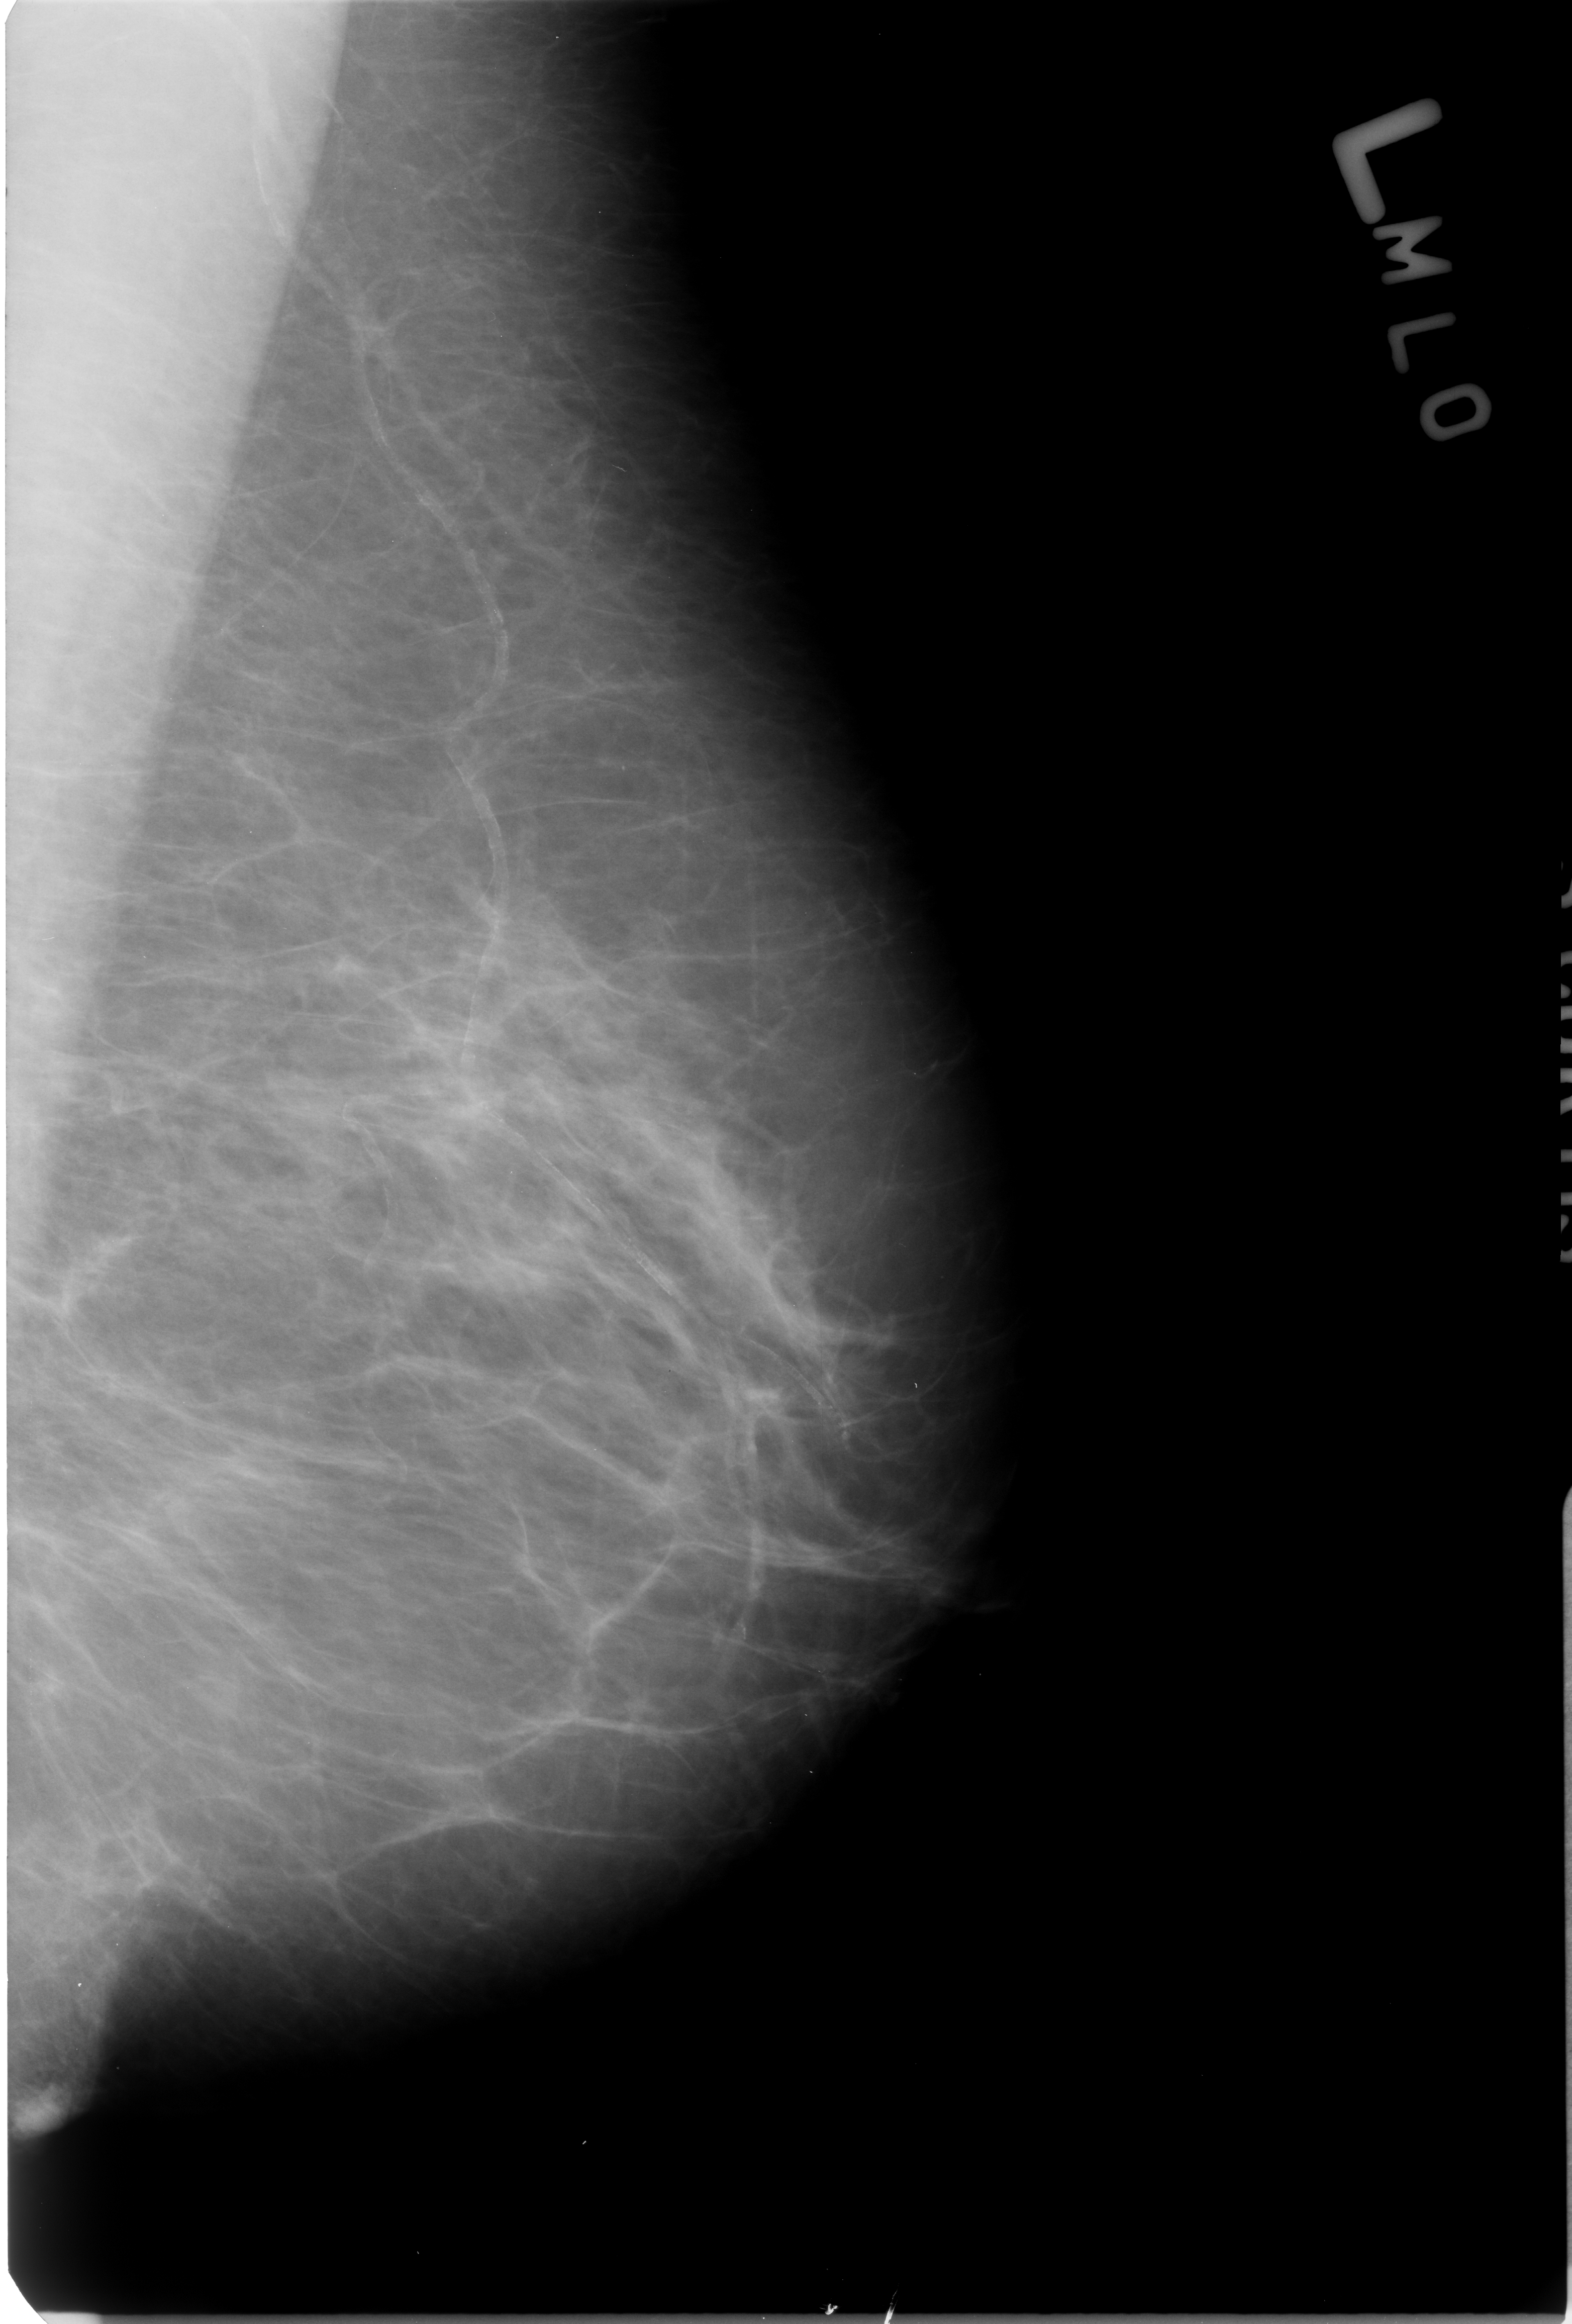
Digitized screen-film mammogram. Left breast. MLO view. BI-RADS breast density category 2 (scale 1–4). 1572 × 2324 image matrix.
Expert-marked regions of interest on this image (one box per marked abnormality):
- Finding 1 of 2: calcifications, morphology vascular; BI-RADS assessment category 2; benign; no additional work-up was recommended (outcome (as recorded, no biopsy): benign without callback): bounding box [x1, y1, x2, y2] px = [297, 1383, 785, 1778]
- Finding 2 of 2: calcifications, morphology vascular; BI-RADS assessment category 2; subtlety rating 3 on a 1 (subtle) to 5 (obvious) scale; outcome (as recorded, no biopsy): benign without callback (not worked up further): [333, 313, 777, 1662]